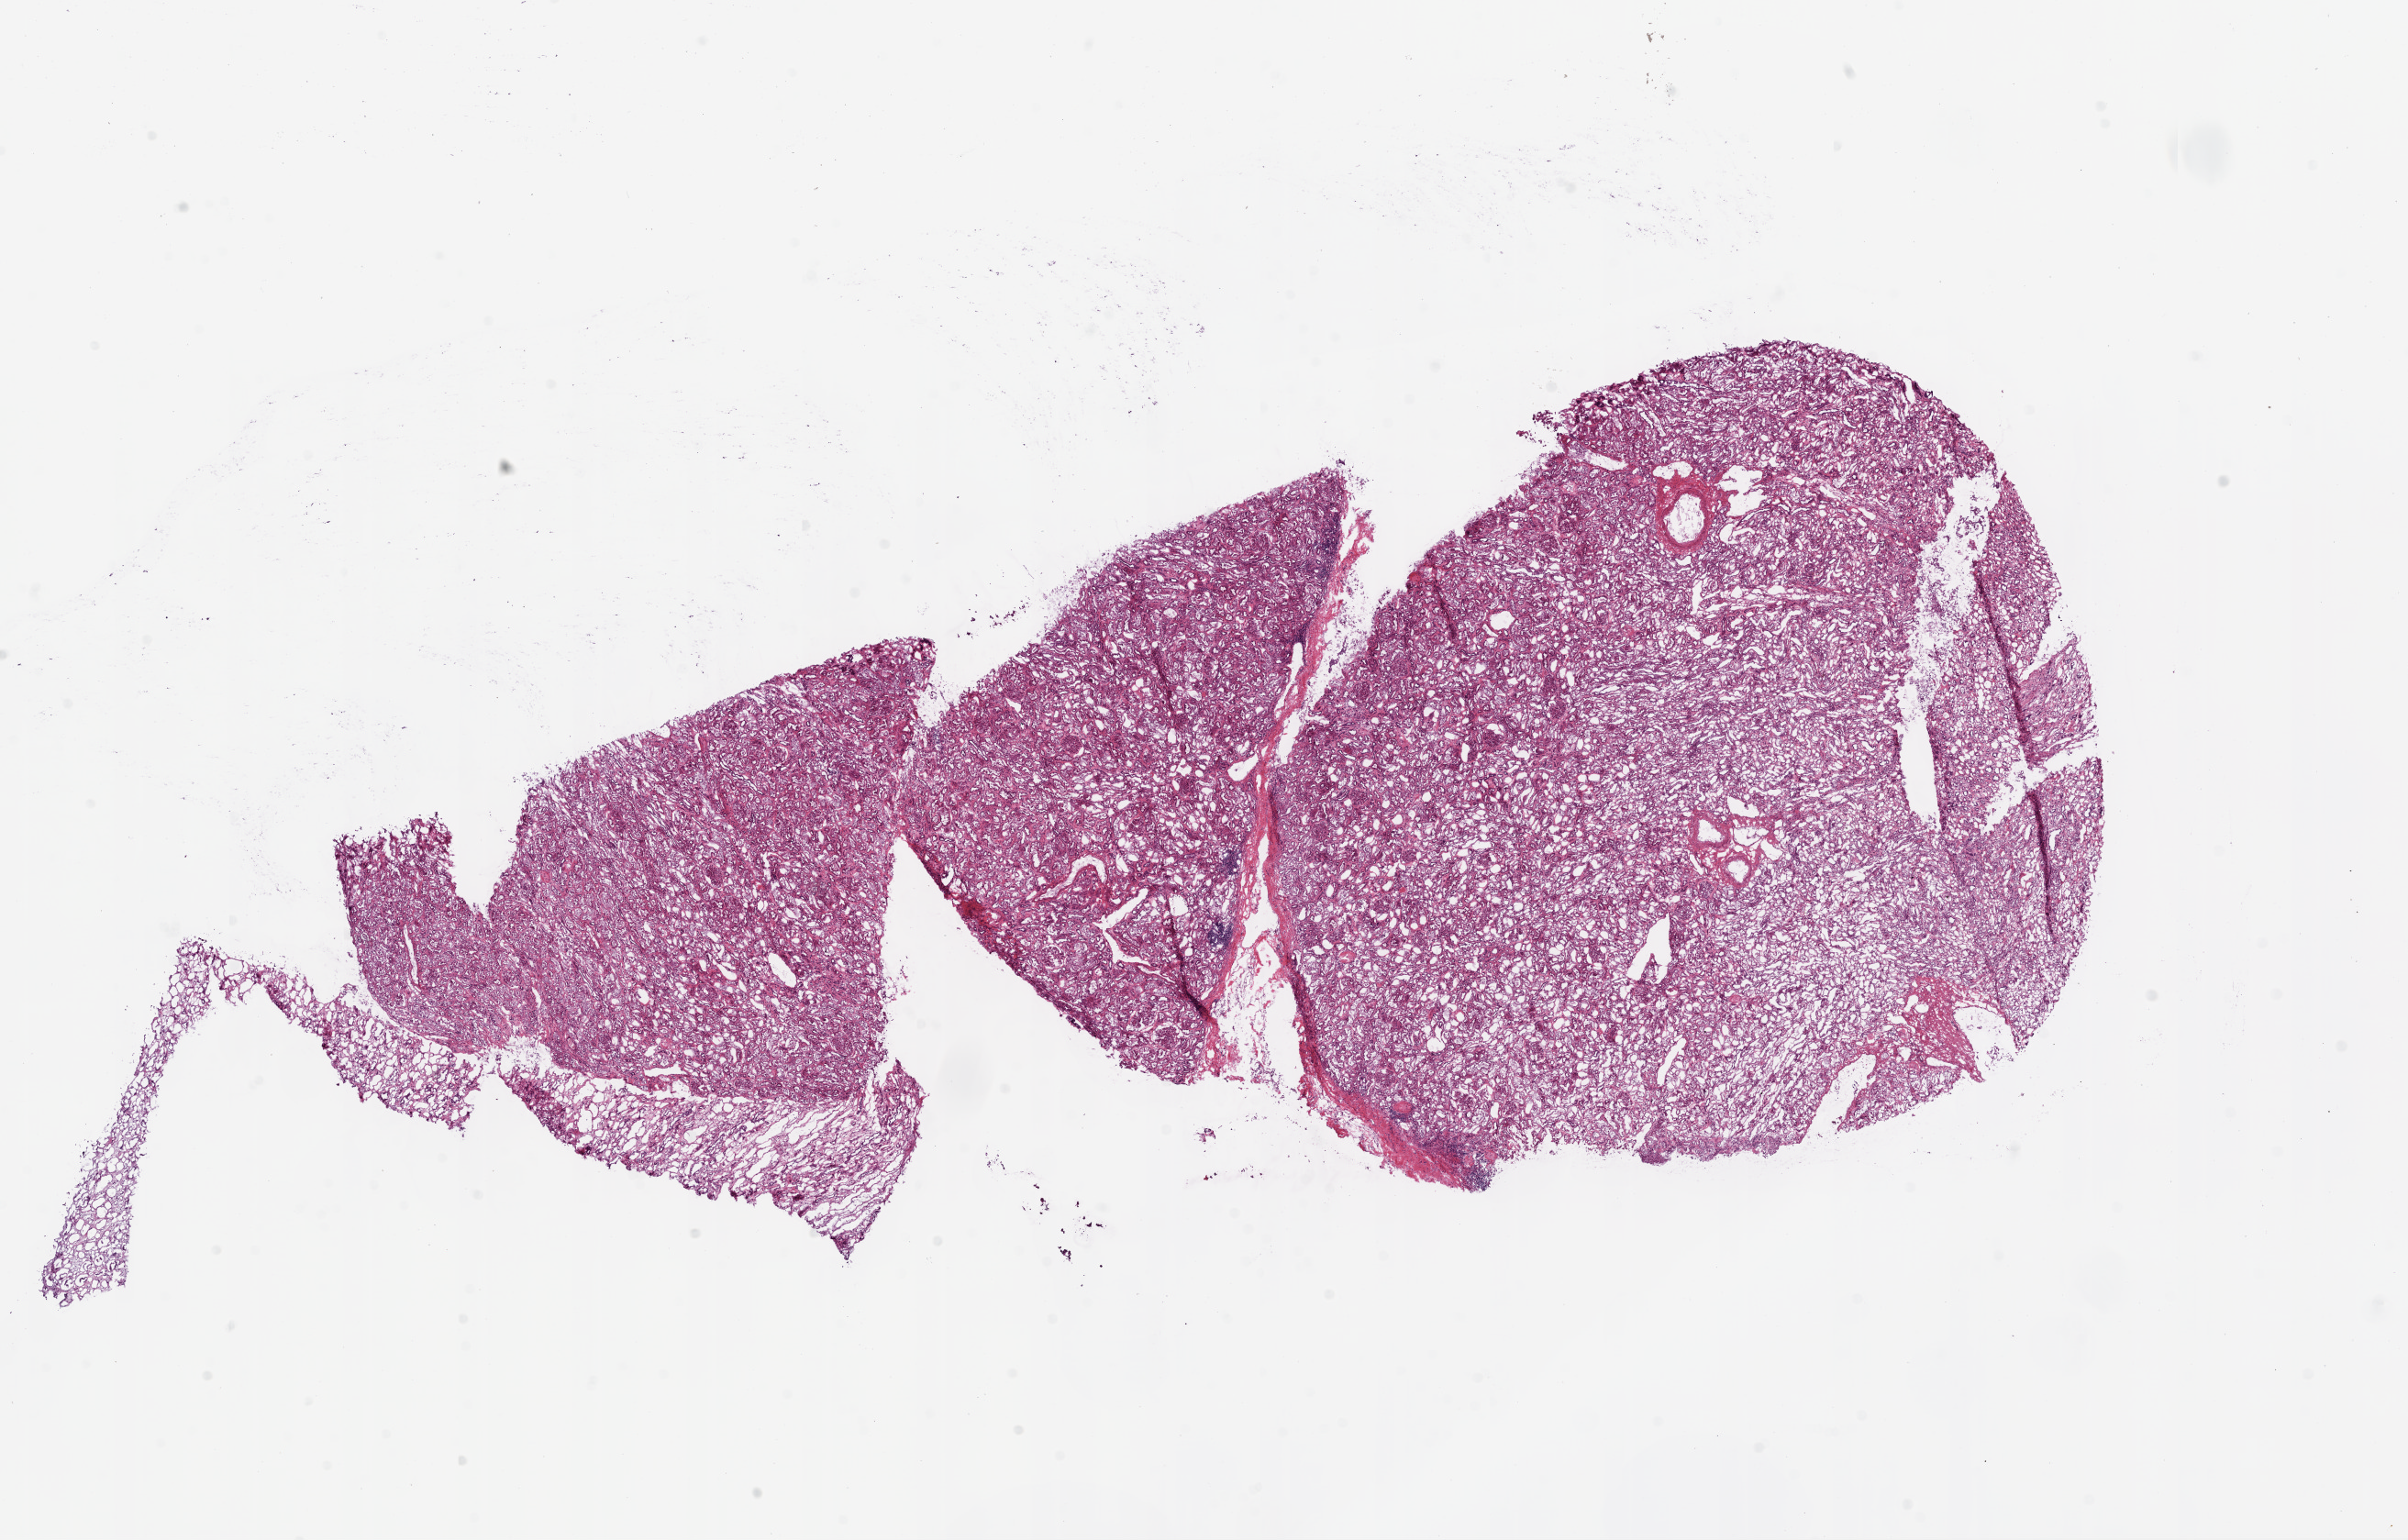
H&E-stained whole-slide image, whole scanned area (about 21.1 x 13.5 mm, from a 20x scan) shown as a low-resolution overview. Frozen section. Solid tissue normal (non-tumour tissue) sample from the kidney. Female patient; age at initial diagnosis 46 years.
This section: solid tissue normal (non-tumour) sample from the same patient. Patient diagnosis: Clear cell adenocarcinoma, NOS.